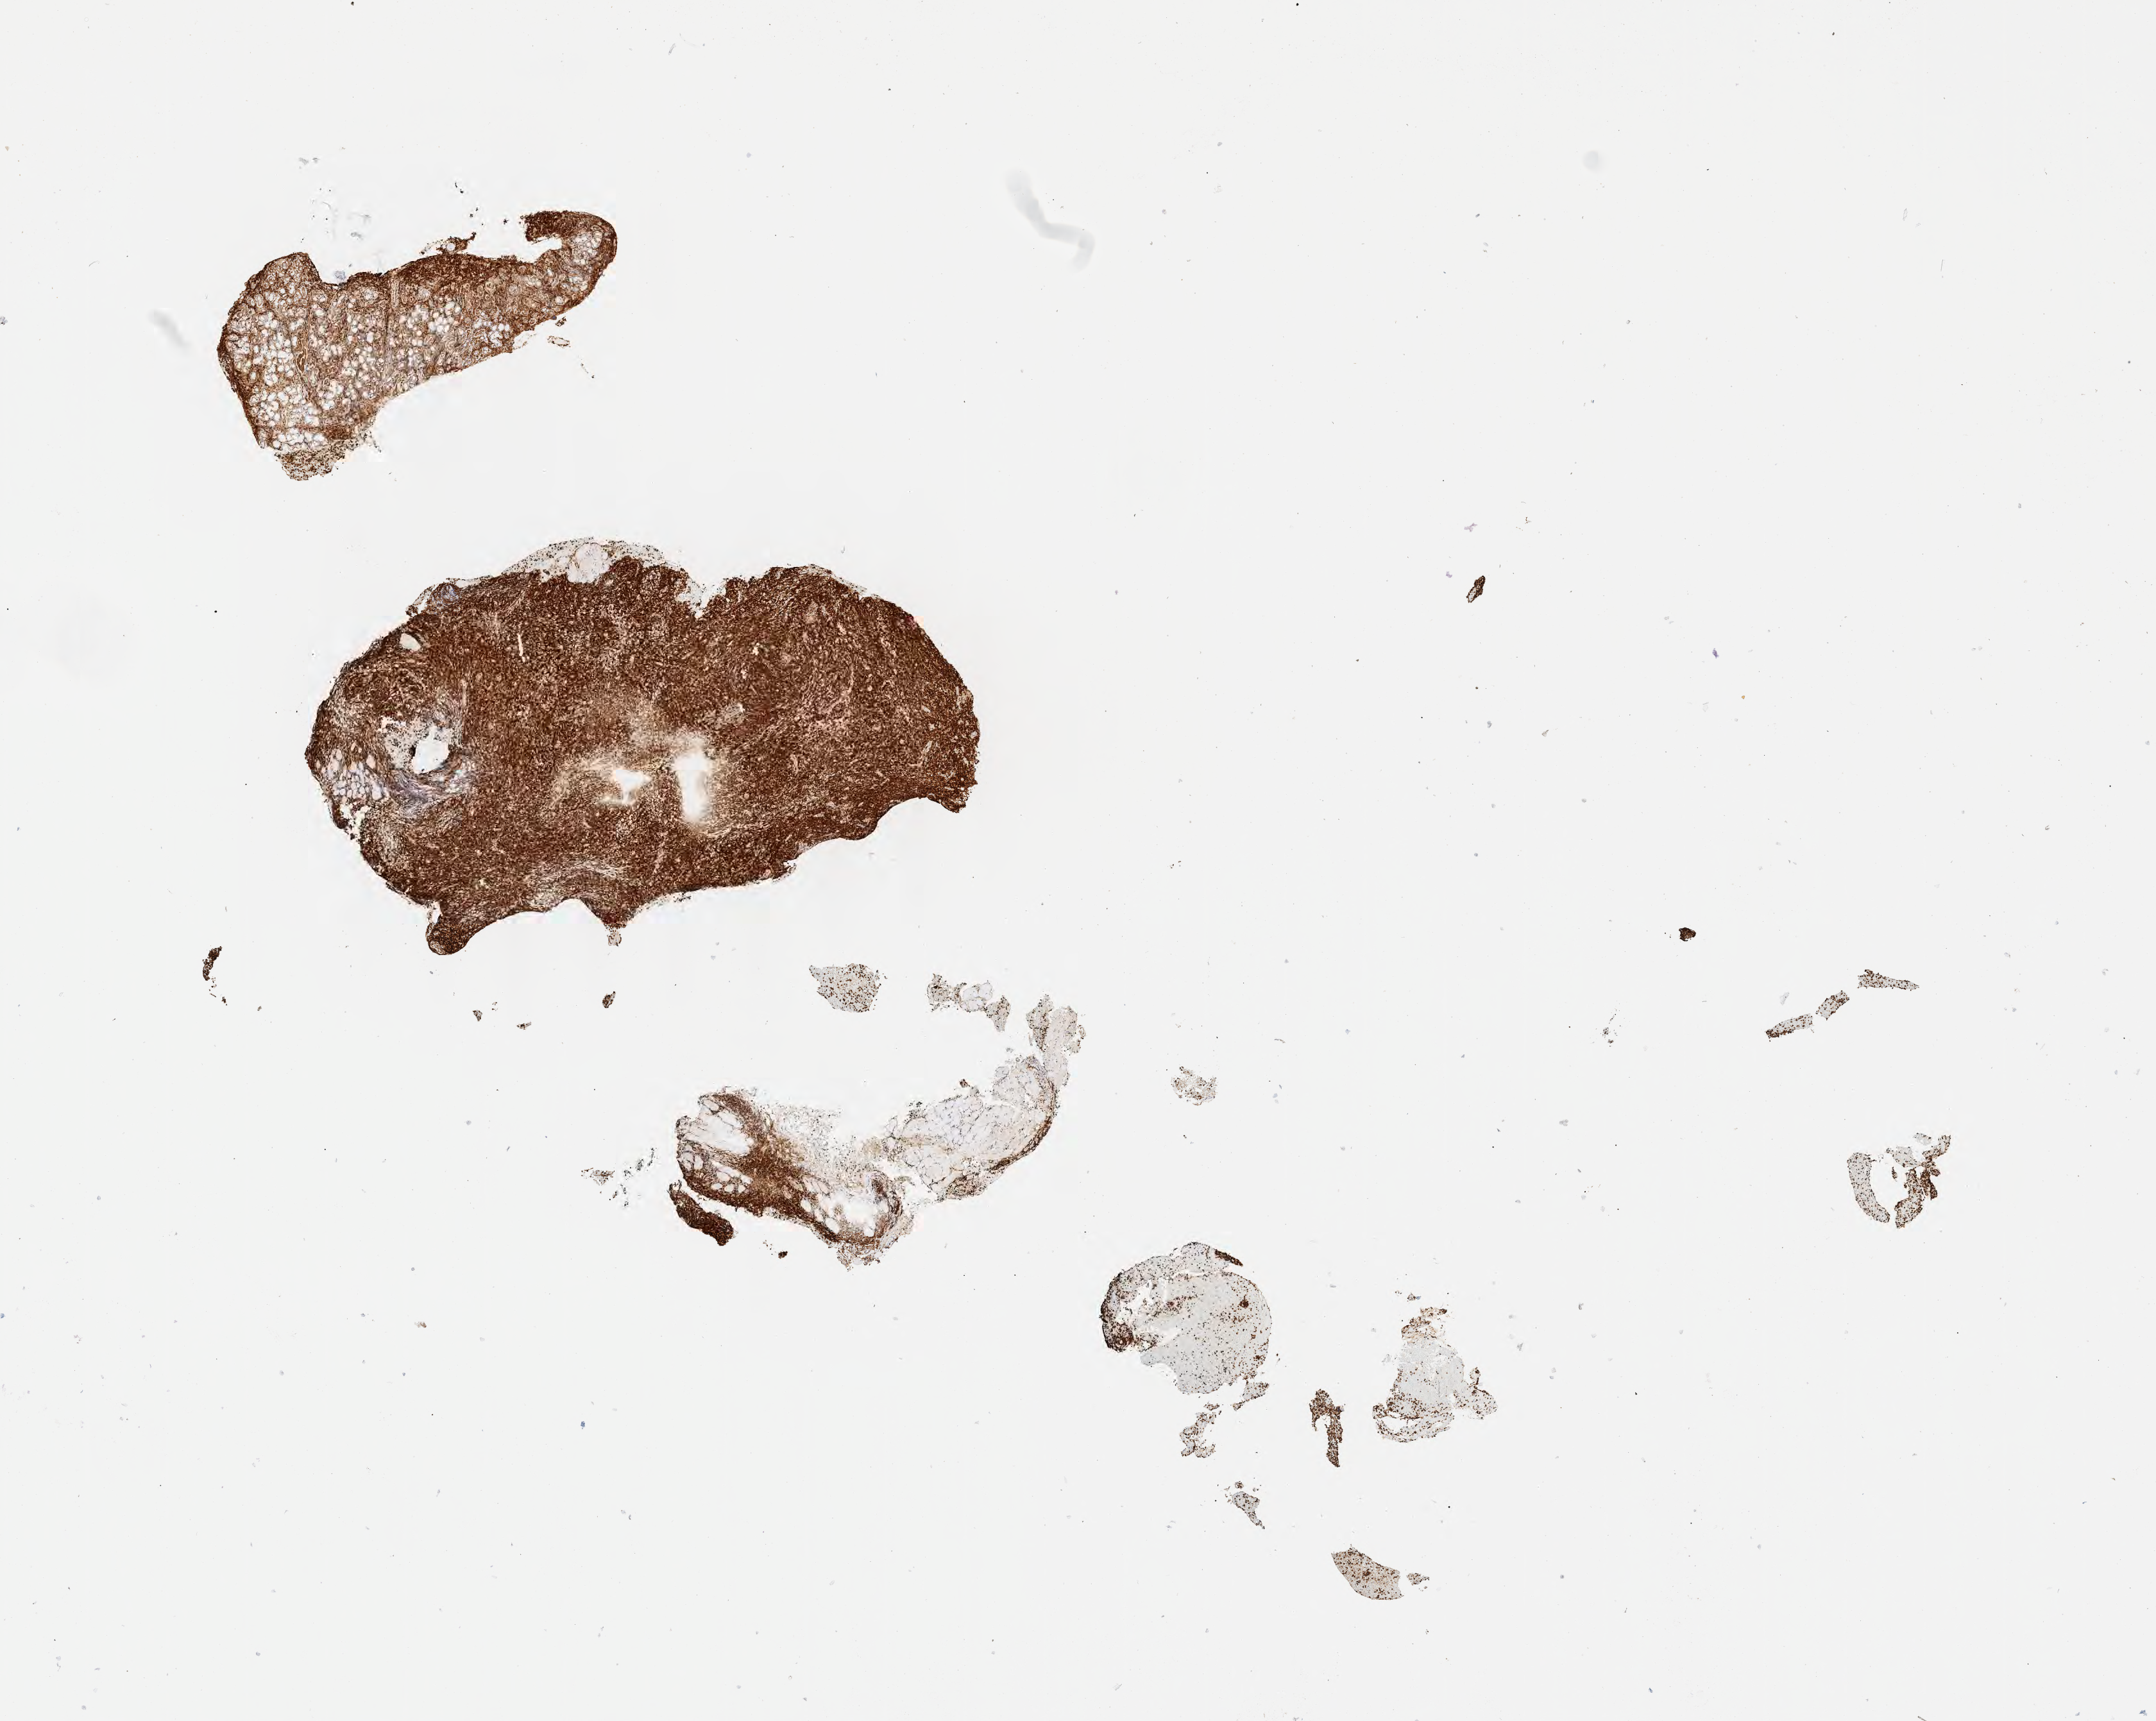
Whole-slide image, immunohistochemical stain for BCL2 — a low-resolution overview of the entire scanned area, about 13.6 x 10.8 mm, specimen: tumor tissue. Patient male; aged 53.
Histologic diagnosis: Diffuse large B-cell lymphoma, NOS.